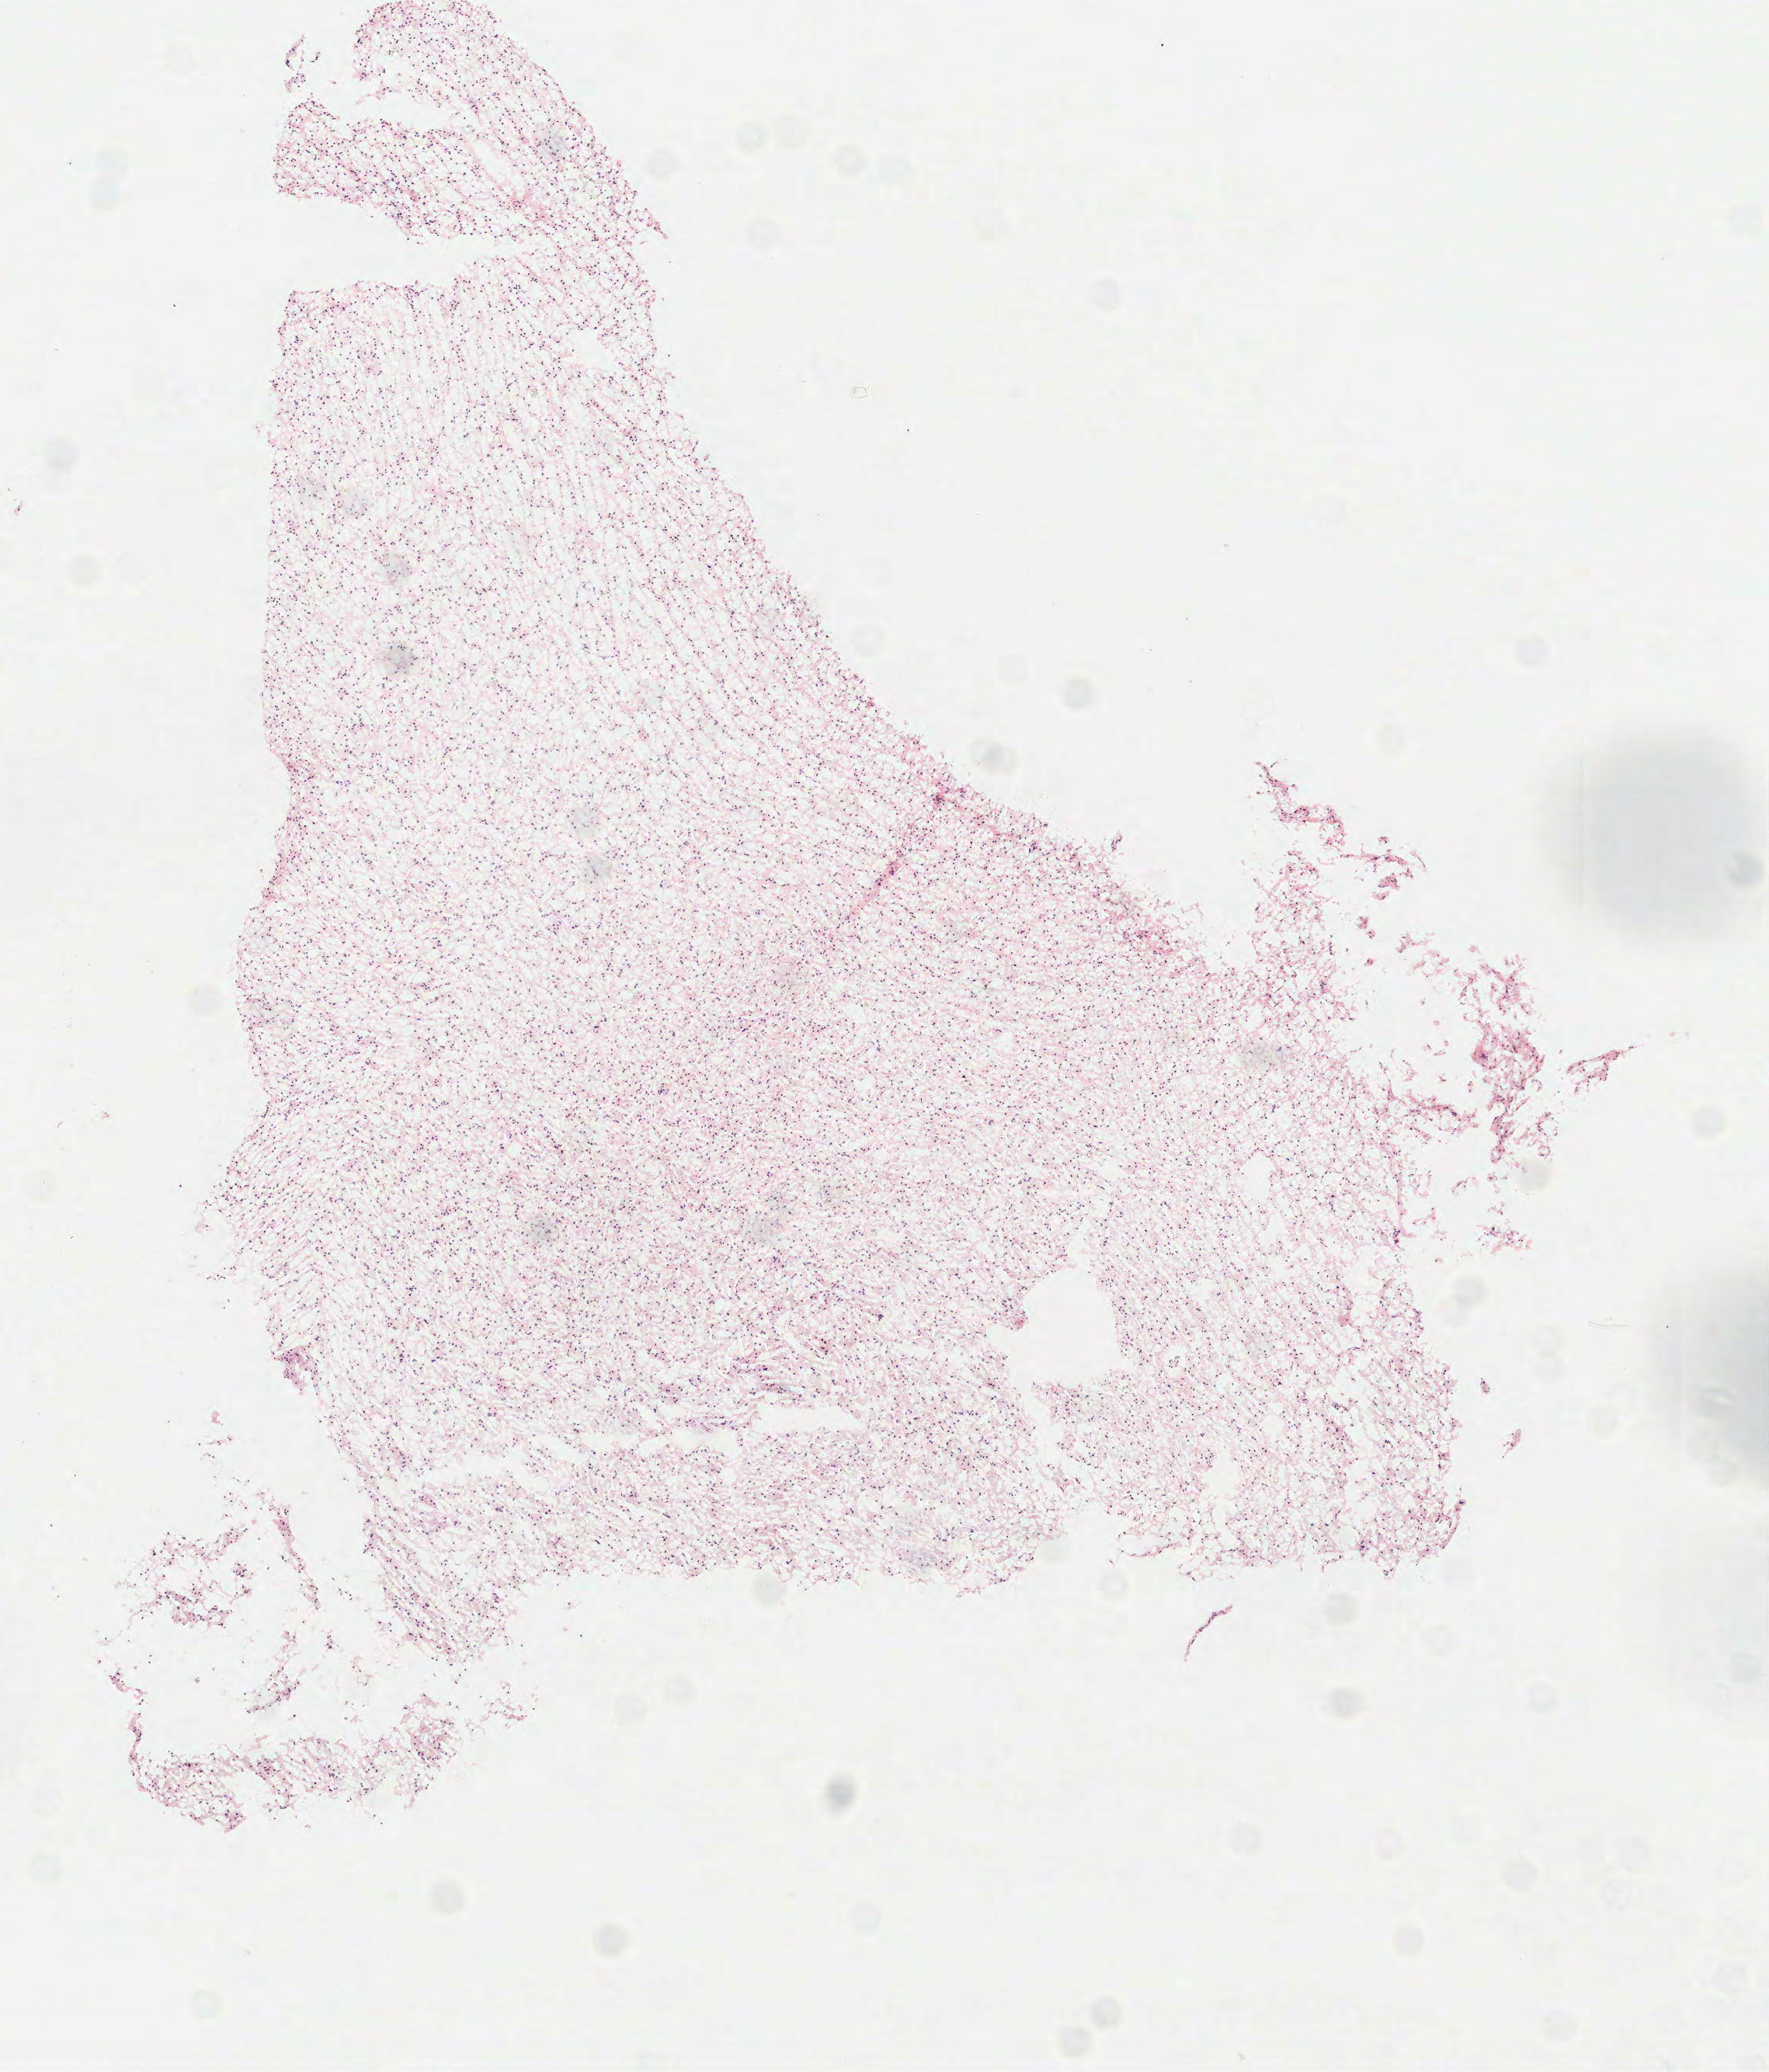
Hematoxylin and eosin (H&E) stained whole-slide image — low-resolution overview of the scanned area, about 4.6 x 5.4 mm (acquisition: 40x scan), formalin-fixed paraffin-embedded (FFPE) diagnostic section, brain, primary tumour sample. Male, age 39 years at initial diagnosis.
* diagnosis: Glioblastoma